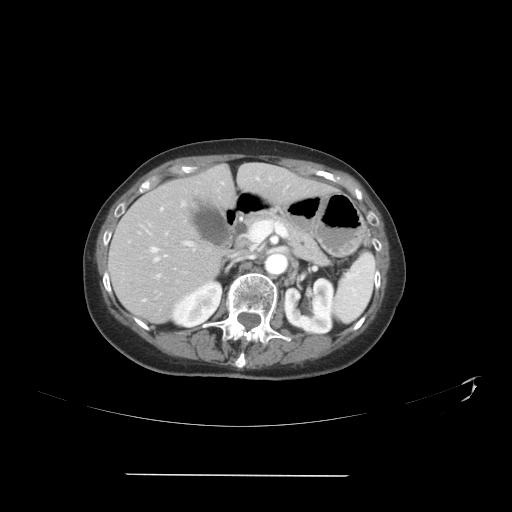
Contrast-enhanced abdominal CT, one axial slice. Position 21 of 41 along the scan axis. Intravenous contrast given. Soft-tissue window (W 400 / L 40 HU). 5 mm slice thickness. 512 × 512 image matrix, field of view 431 × 431 mm. Female patient, age 74 years. From the clinical record (not read from this slice): diagnosis: colorectal cancer liver metastases, imaged before liver resection.
Annotated regions visible in this slice (expert manual segmentation):
- hepatic veins: bounding box <143,201,185,302> (left, top, right, bottom; pixels)
- liver: <110,164,328,322>
- planned liver remnant (the part of the liver to remain after resection): <117,164,325,246>
- portal vein (with intrahepatic branches): <160,207,195,250>